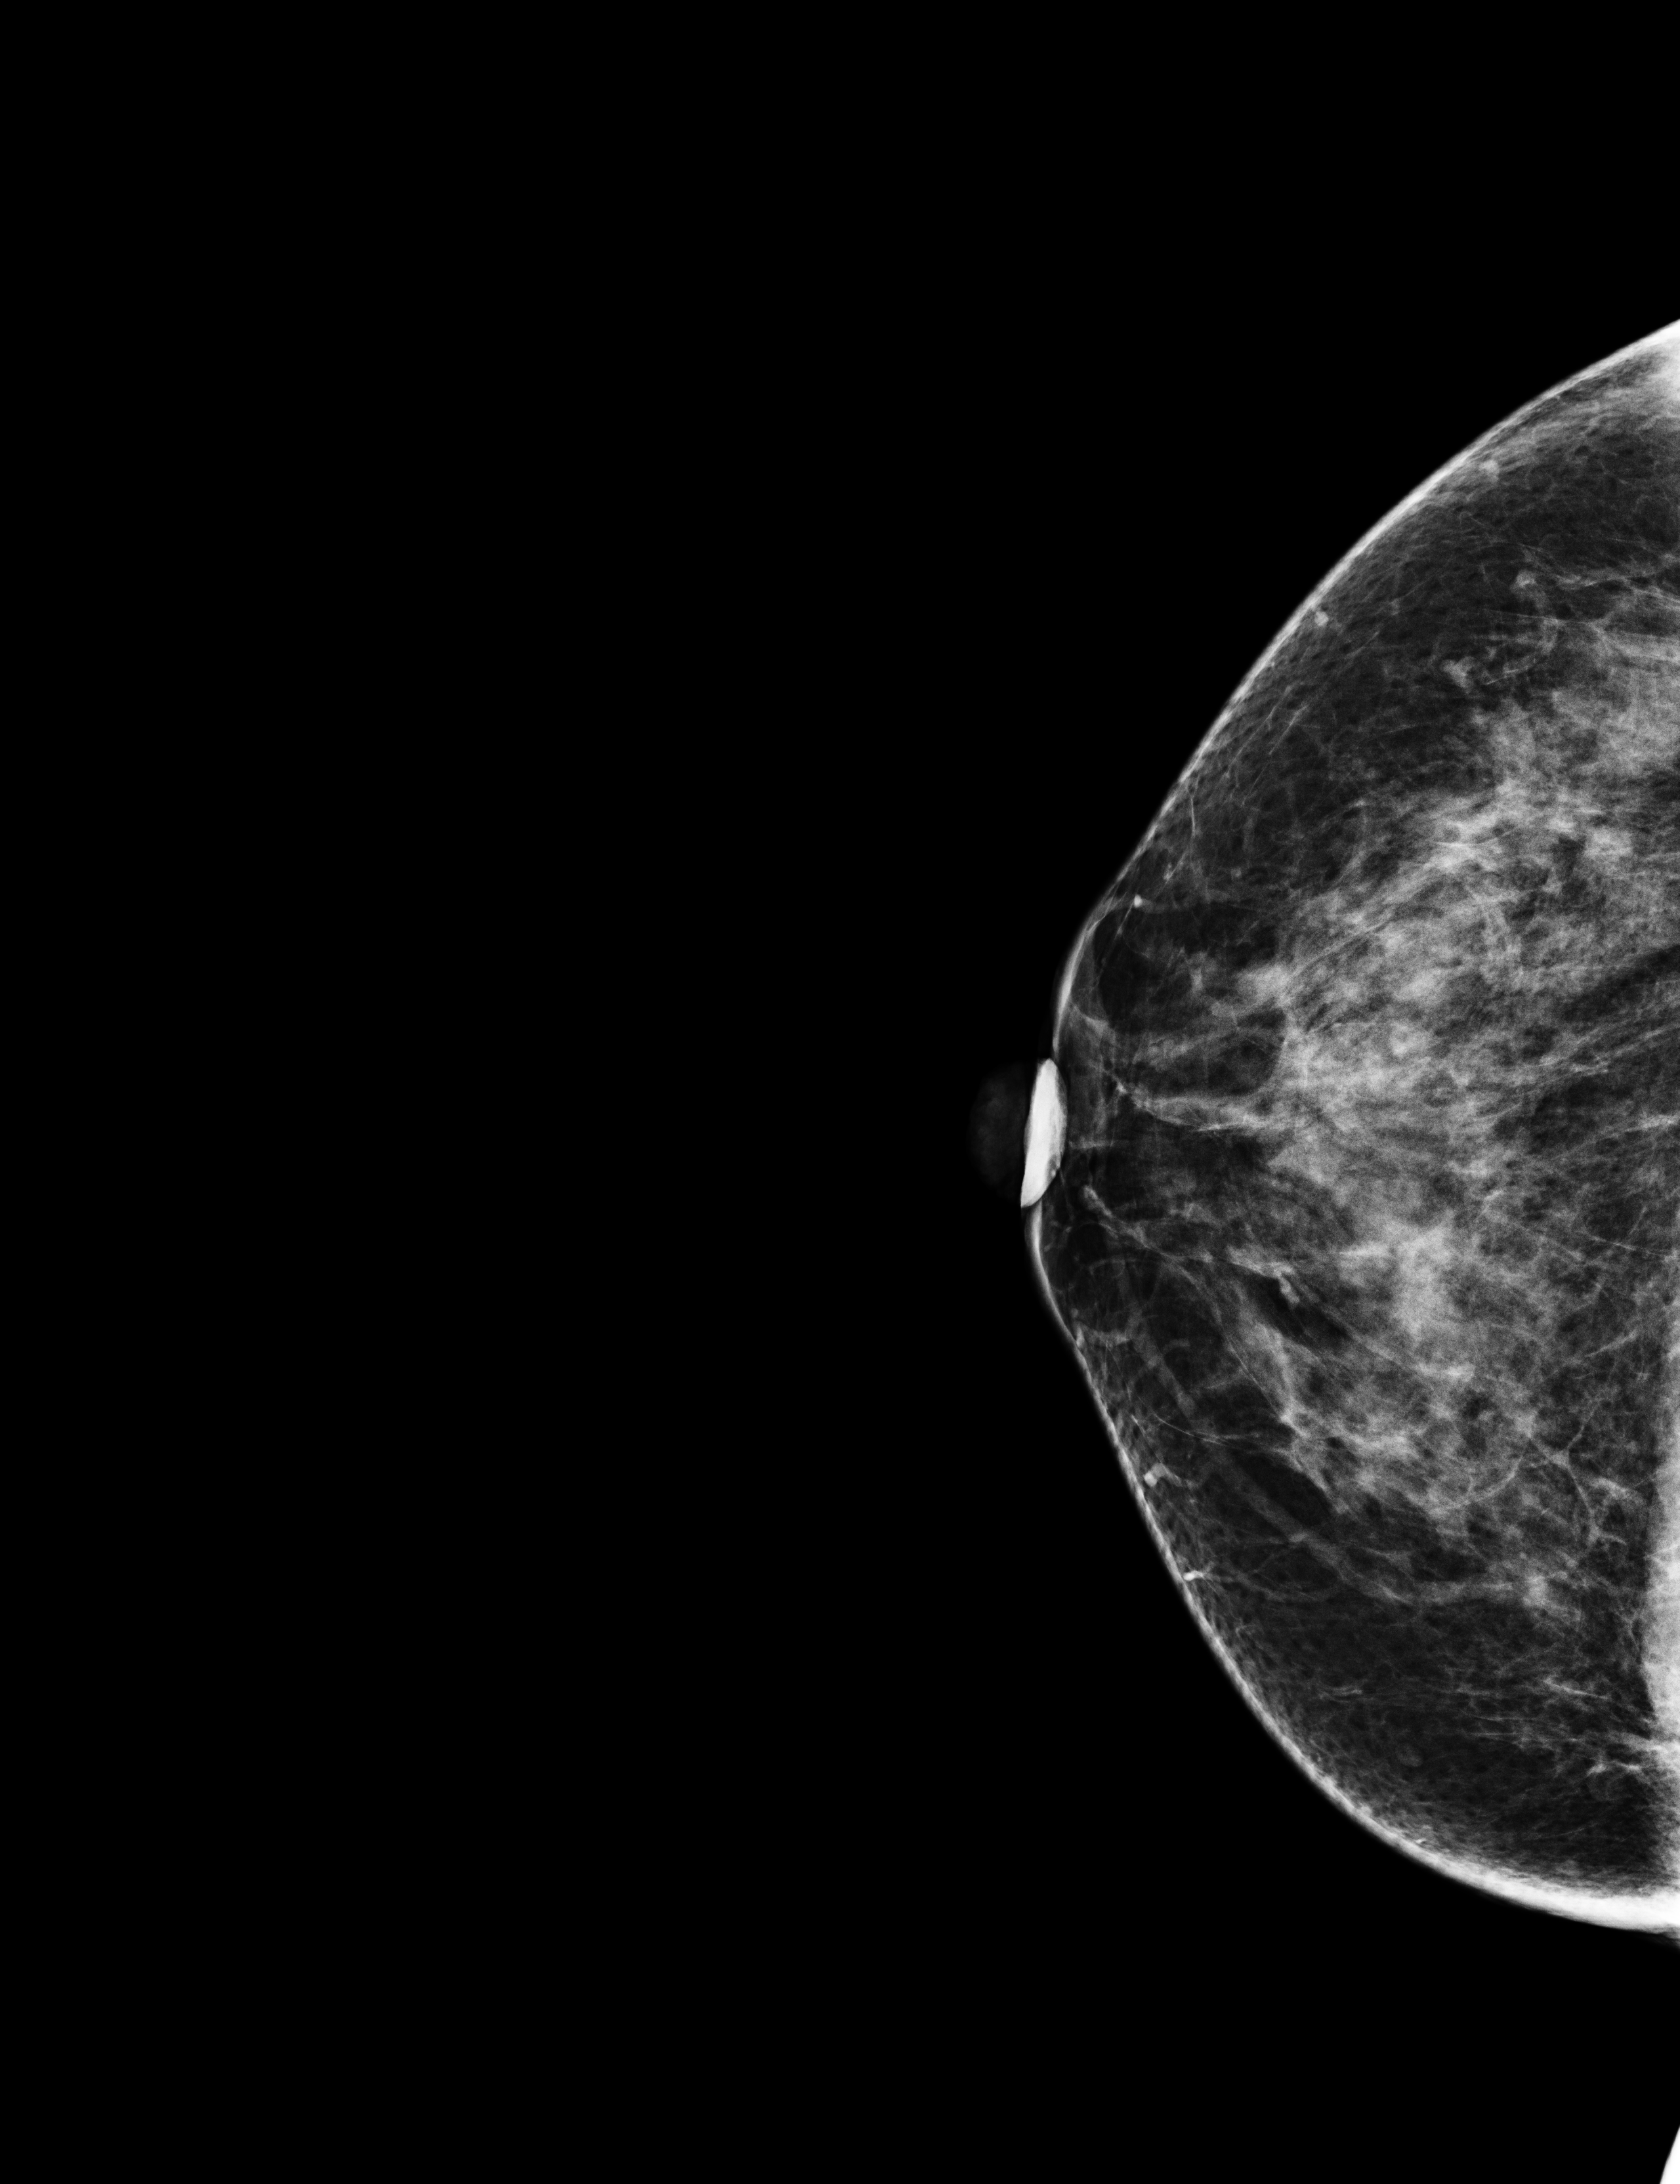
Screening examination. Female patient, age 62 years.
Image type: full-field digital mammogram. Breast: right. Projection: cranio-caudal projection.